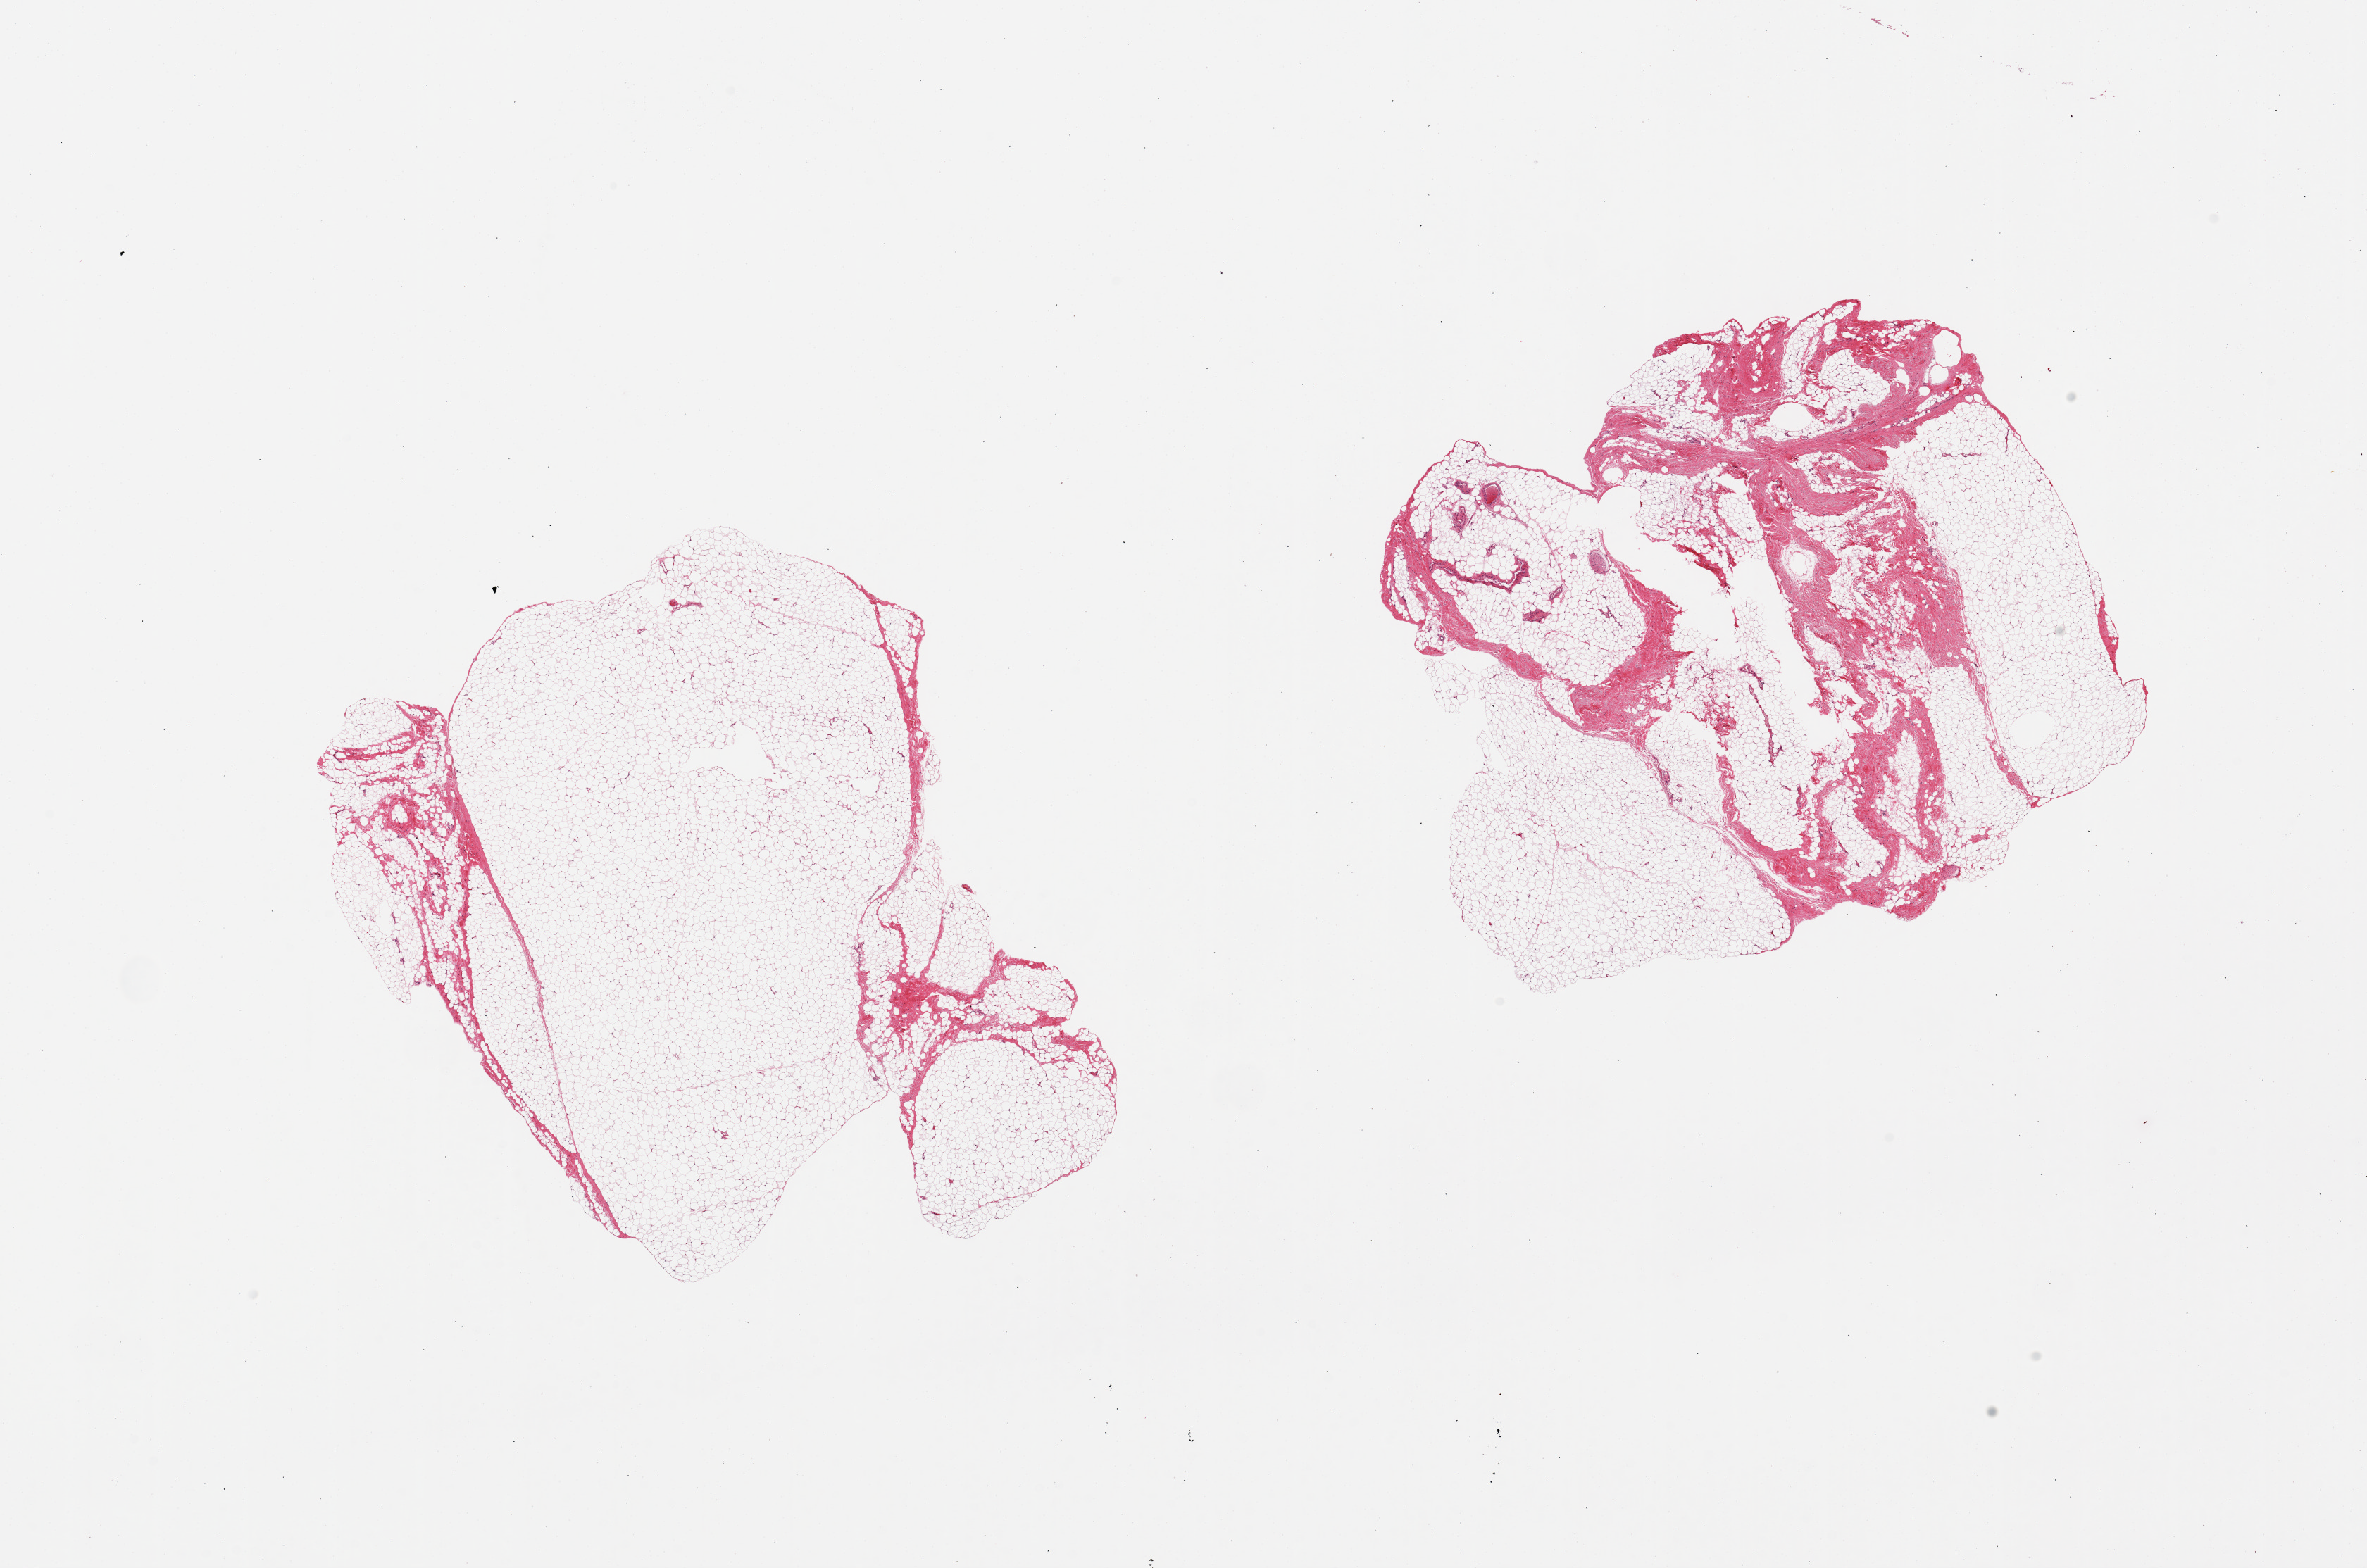
Whole-slide image, haematoxylin and eosin stain — a low-resolution overview of the entire scanned area, about 26.6 x 17.6 mm. PAXgene-fixed, paraffin-embedded tissue. Section of breast (target tissue). Tissue donor sample.
- review note (as recorded): 2 pieces; fibroadipose with no mammary ducts